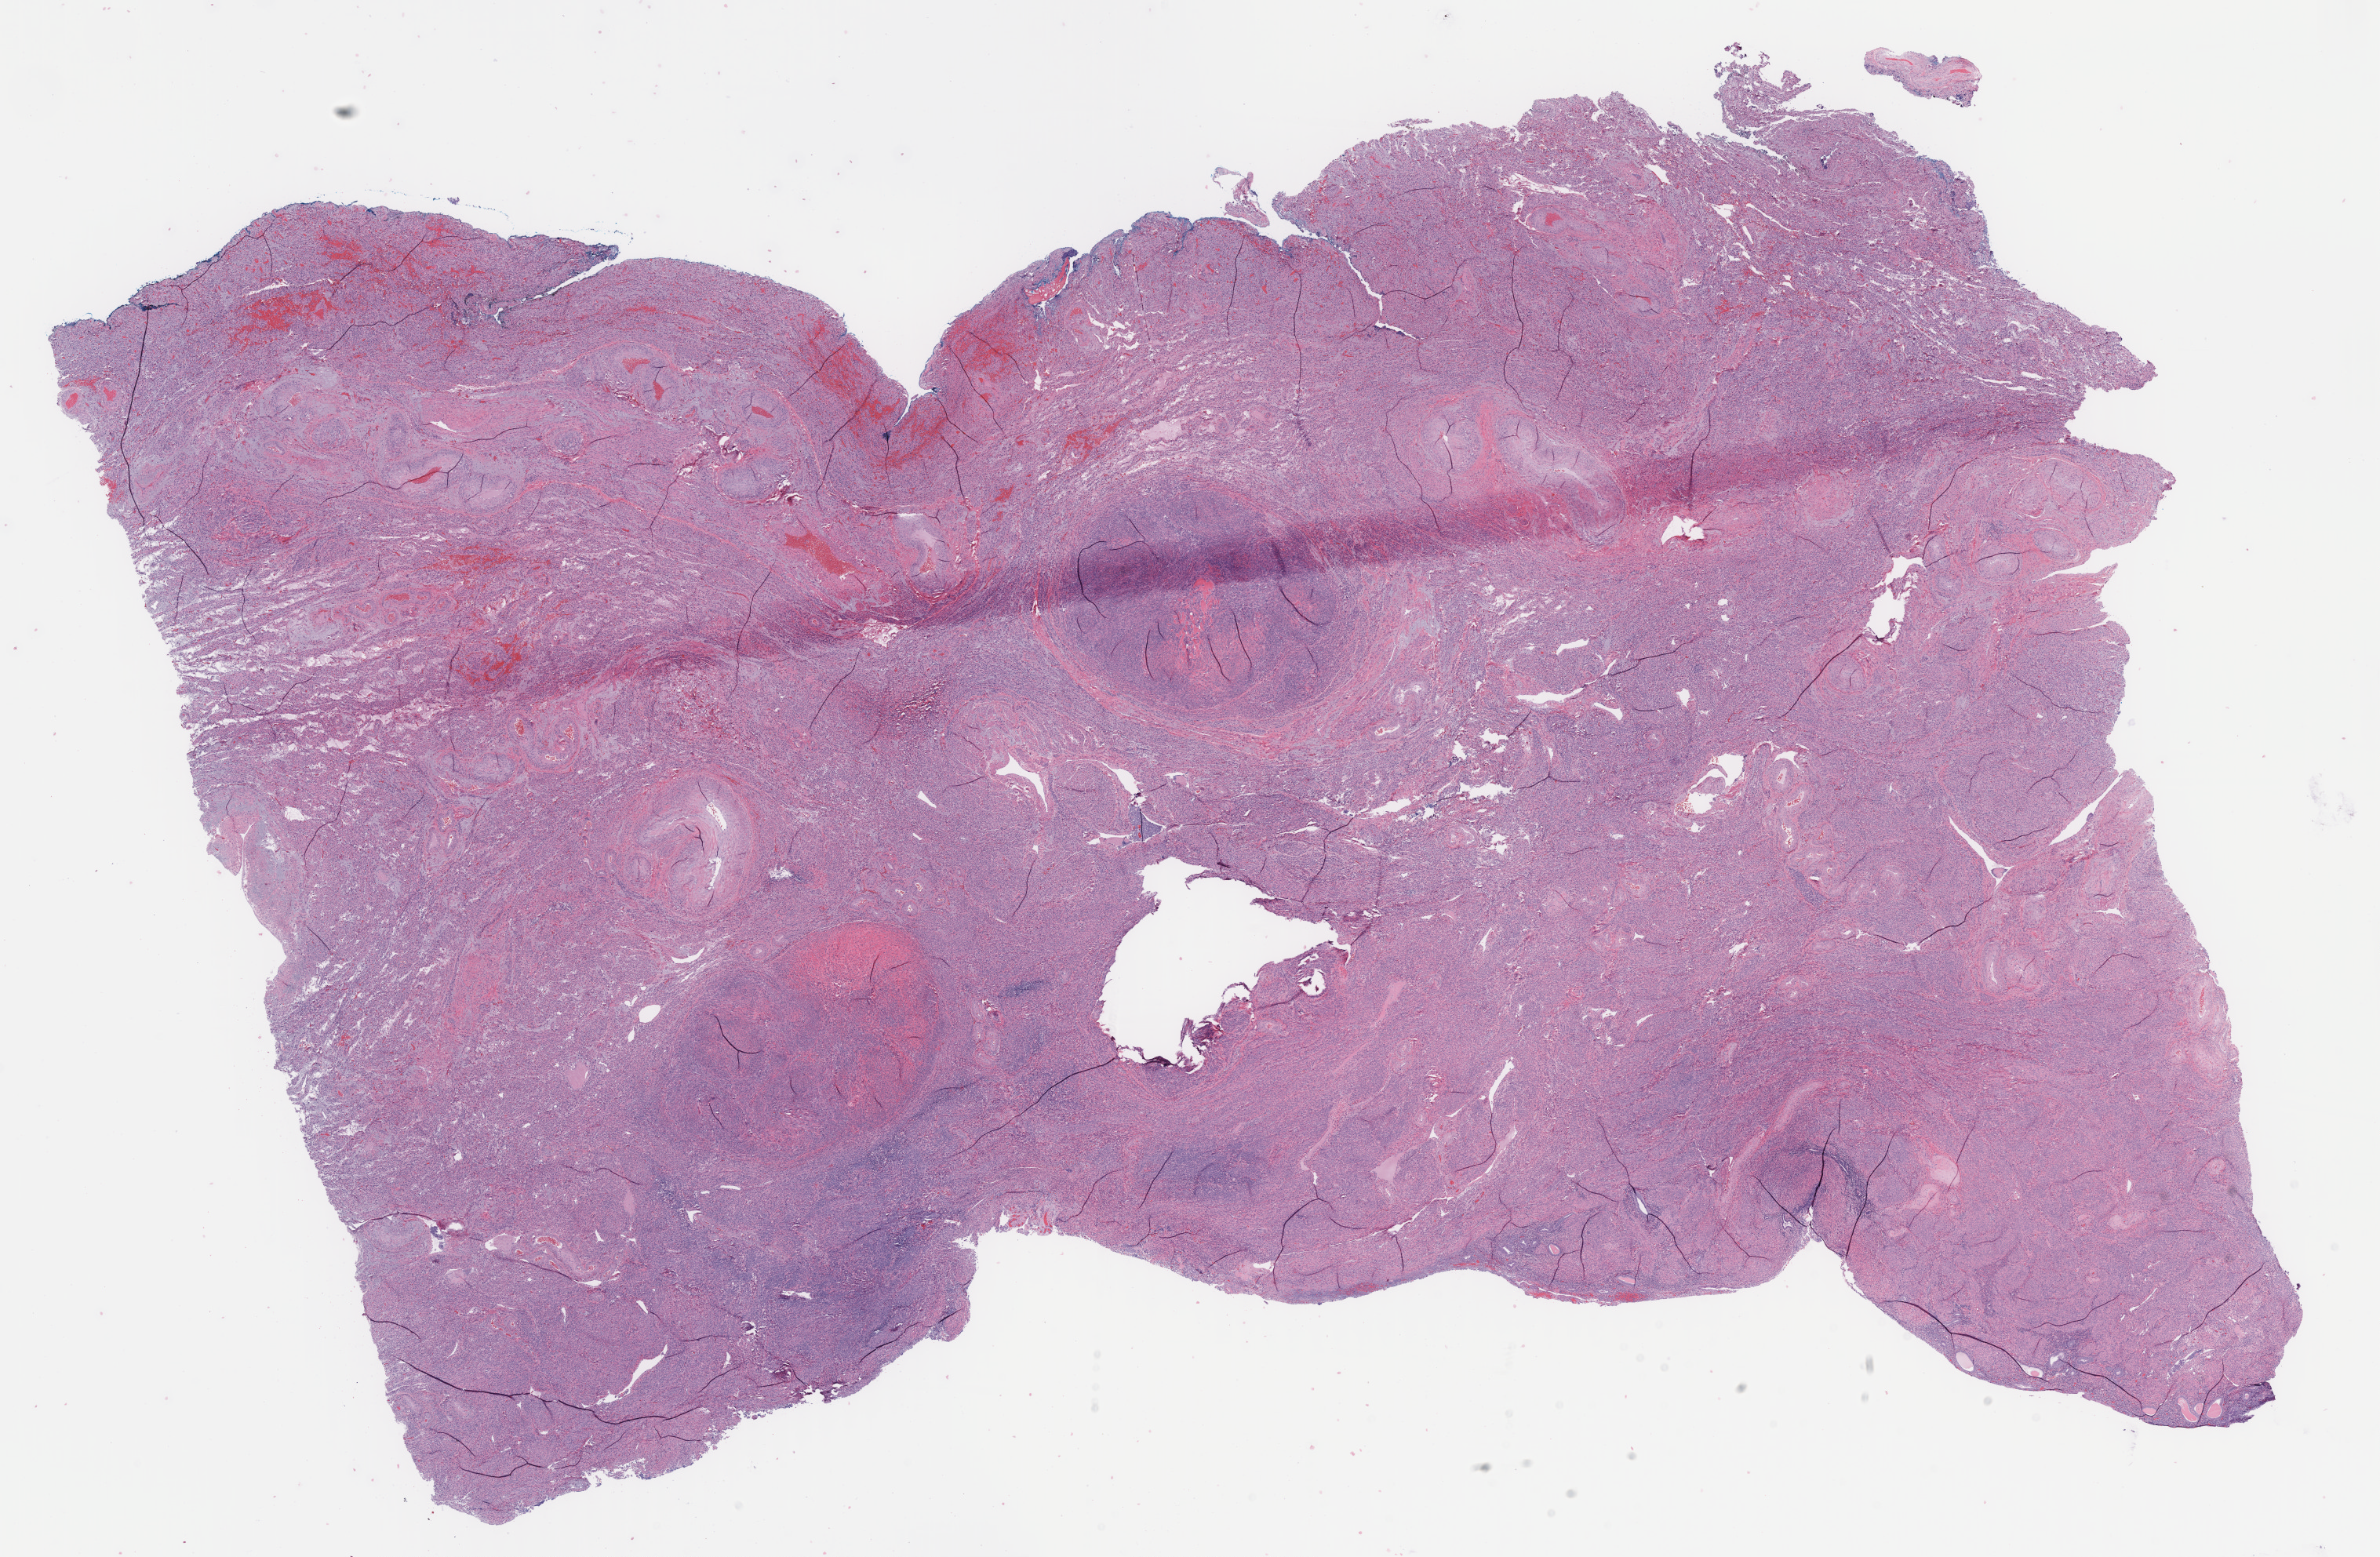
Digitized hematoxylin and eosin (H&E)-stained section, low-resolution overview of the scanned area, about 24.0 x 15.7 mm. Frozen section (tissue freezing medium). Specimen: non-tumor (normal tissue) sample from a patient with high grade serous carcinoma. Anatomic site: endometrium. Female patient. Pathologist review of this section (percent, as recorded): tumor cells 0%, tumor nuclei 0%, stromal cells 85%, necrosis 0%, normal cells 15%. Infiltration values recorded for this section: lymphocyte infiltration 6%, monocyte infiltration 3%, neutrophil infiltration 8%.
This section: non-tumor tissue sample; the patient's diagnosis is given above.